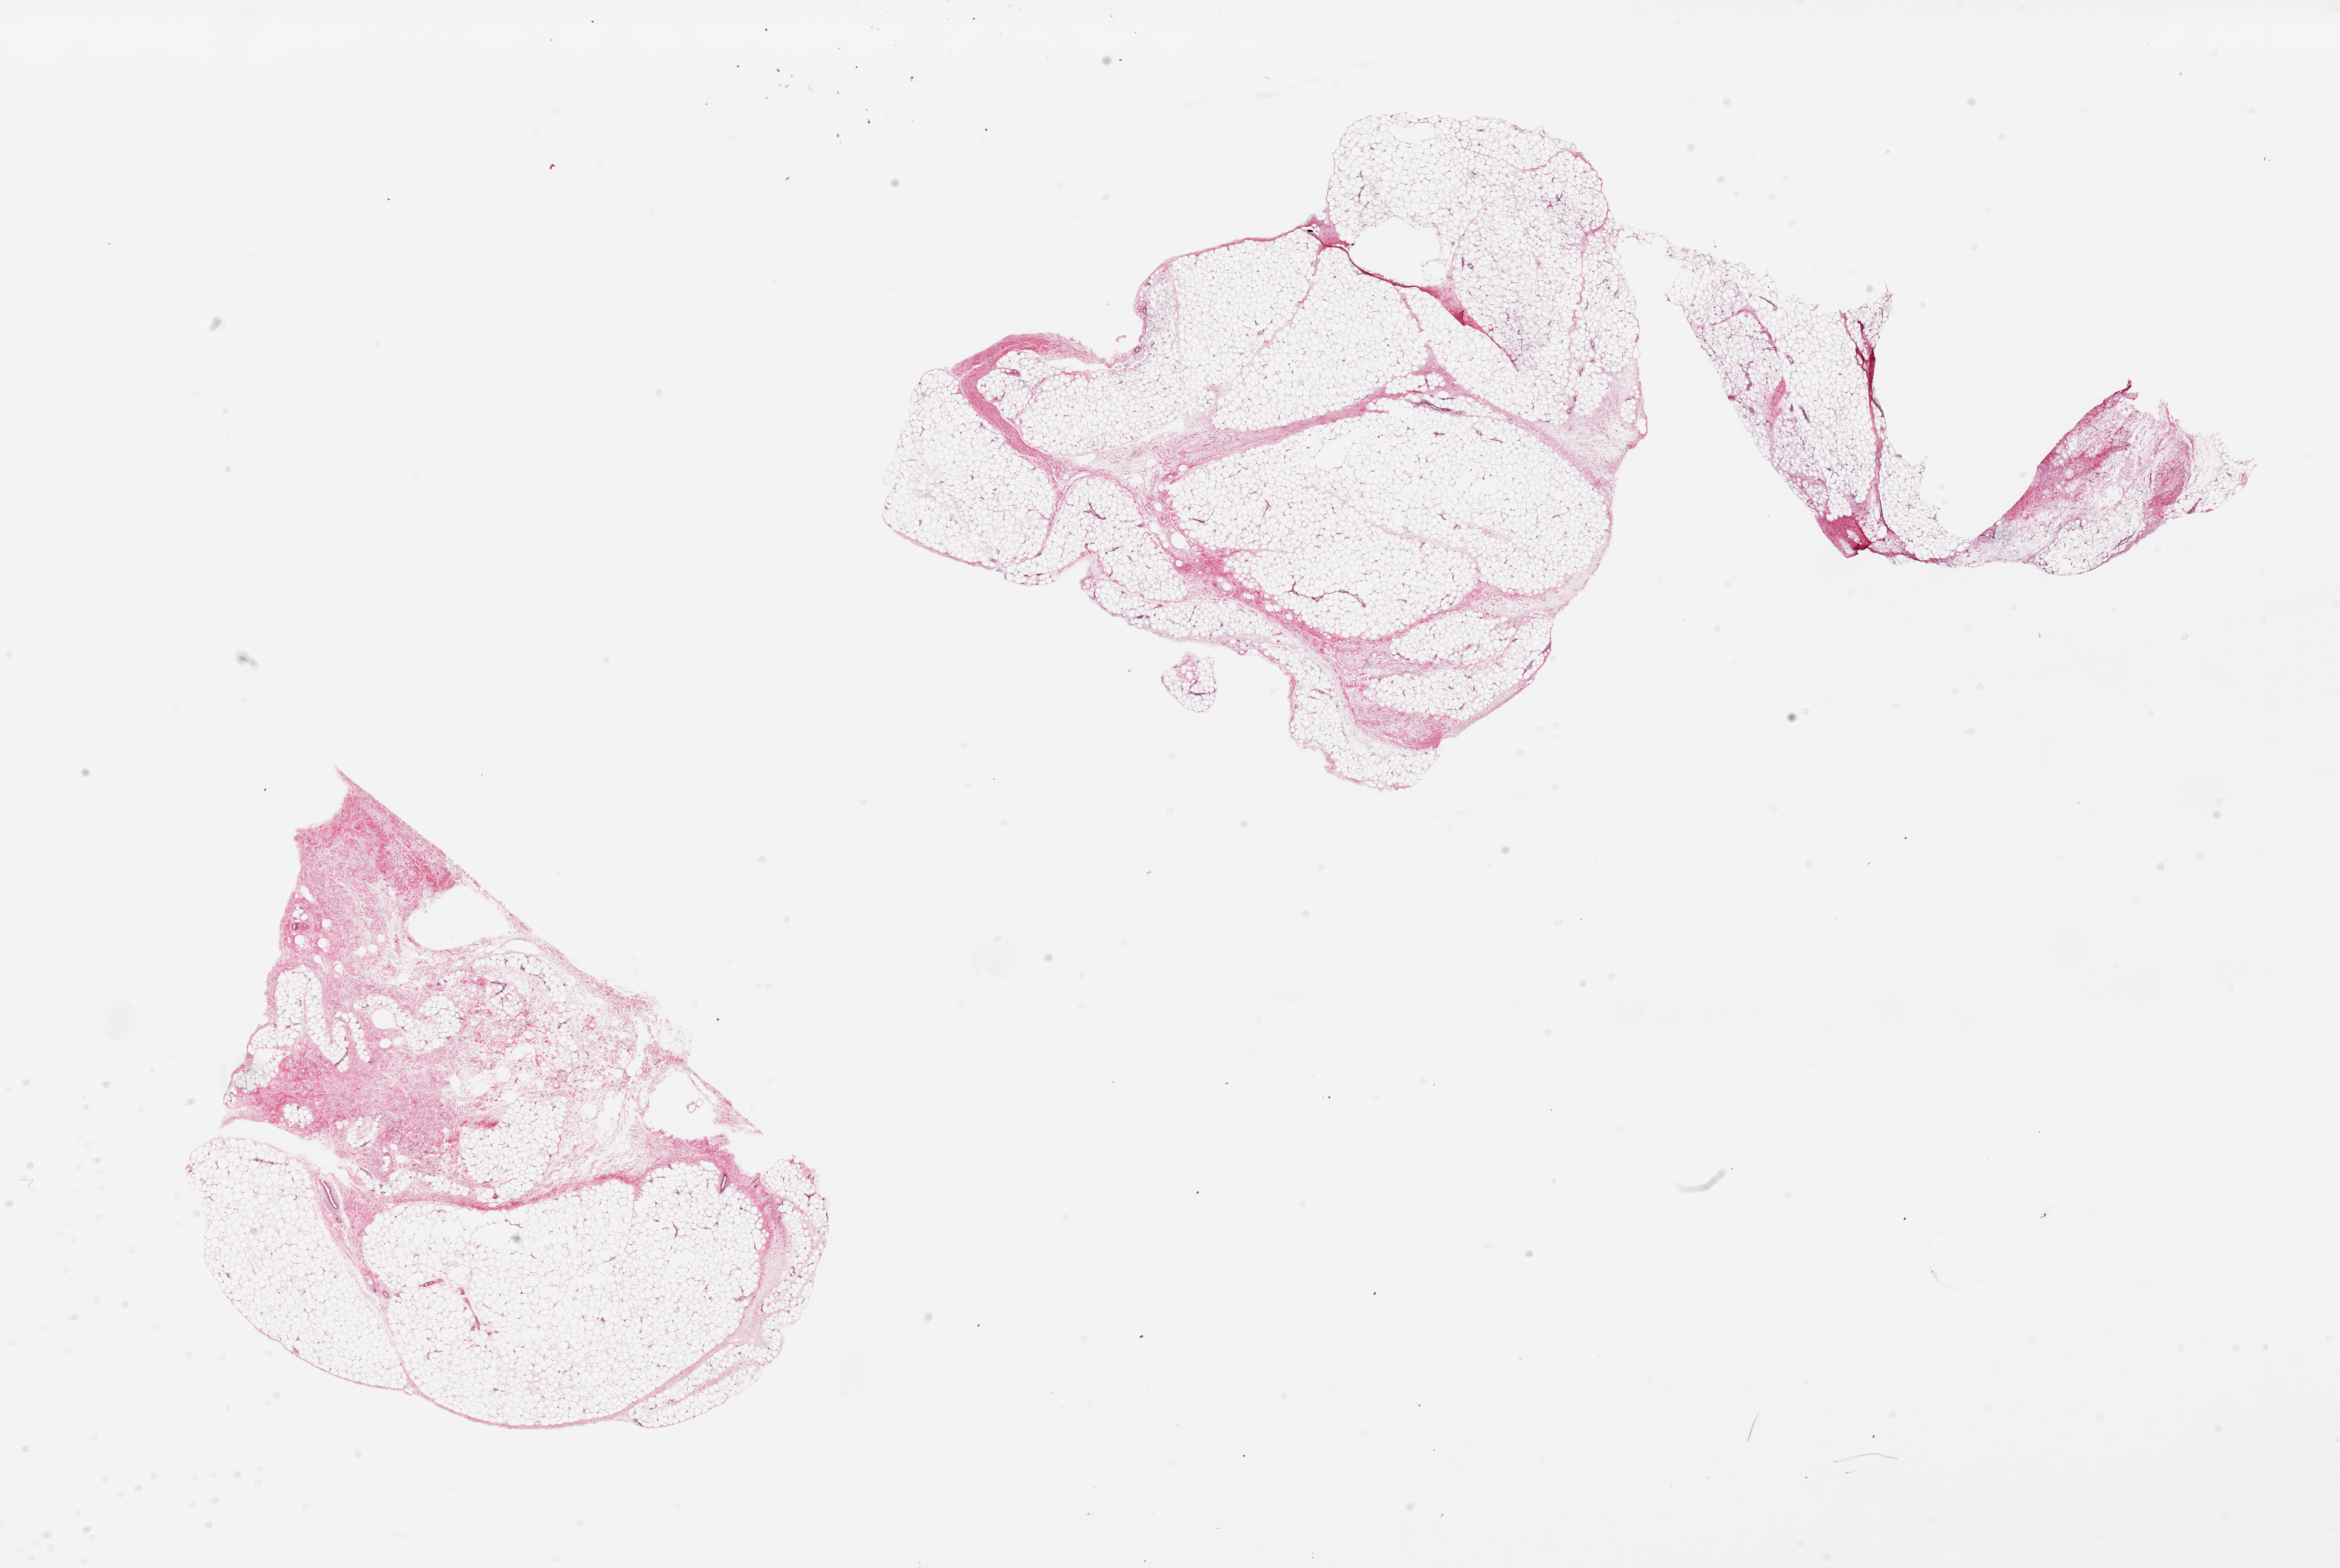
Digitized hematoxylin and eosin (H&E)-stained section, brightfield — whole scanned area (about 30.5 x 20.5 mm, acquisition: 20x scan) shown as a low-resolution overview. PAXgene-fixed paraffin-embedded (PFPE) section. Section of adipose tissue (target tissue). Tissue donor sample. Donor sex: male.
Reviewer comment on this tissue sample: 2 pieces, 9x6.5 and 18x9mm; ~25-30% fibrous tissue/bands.